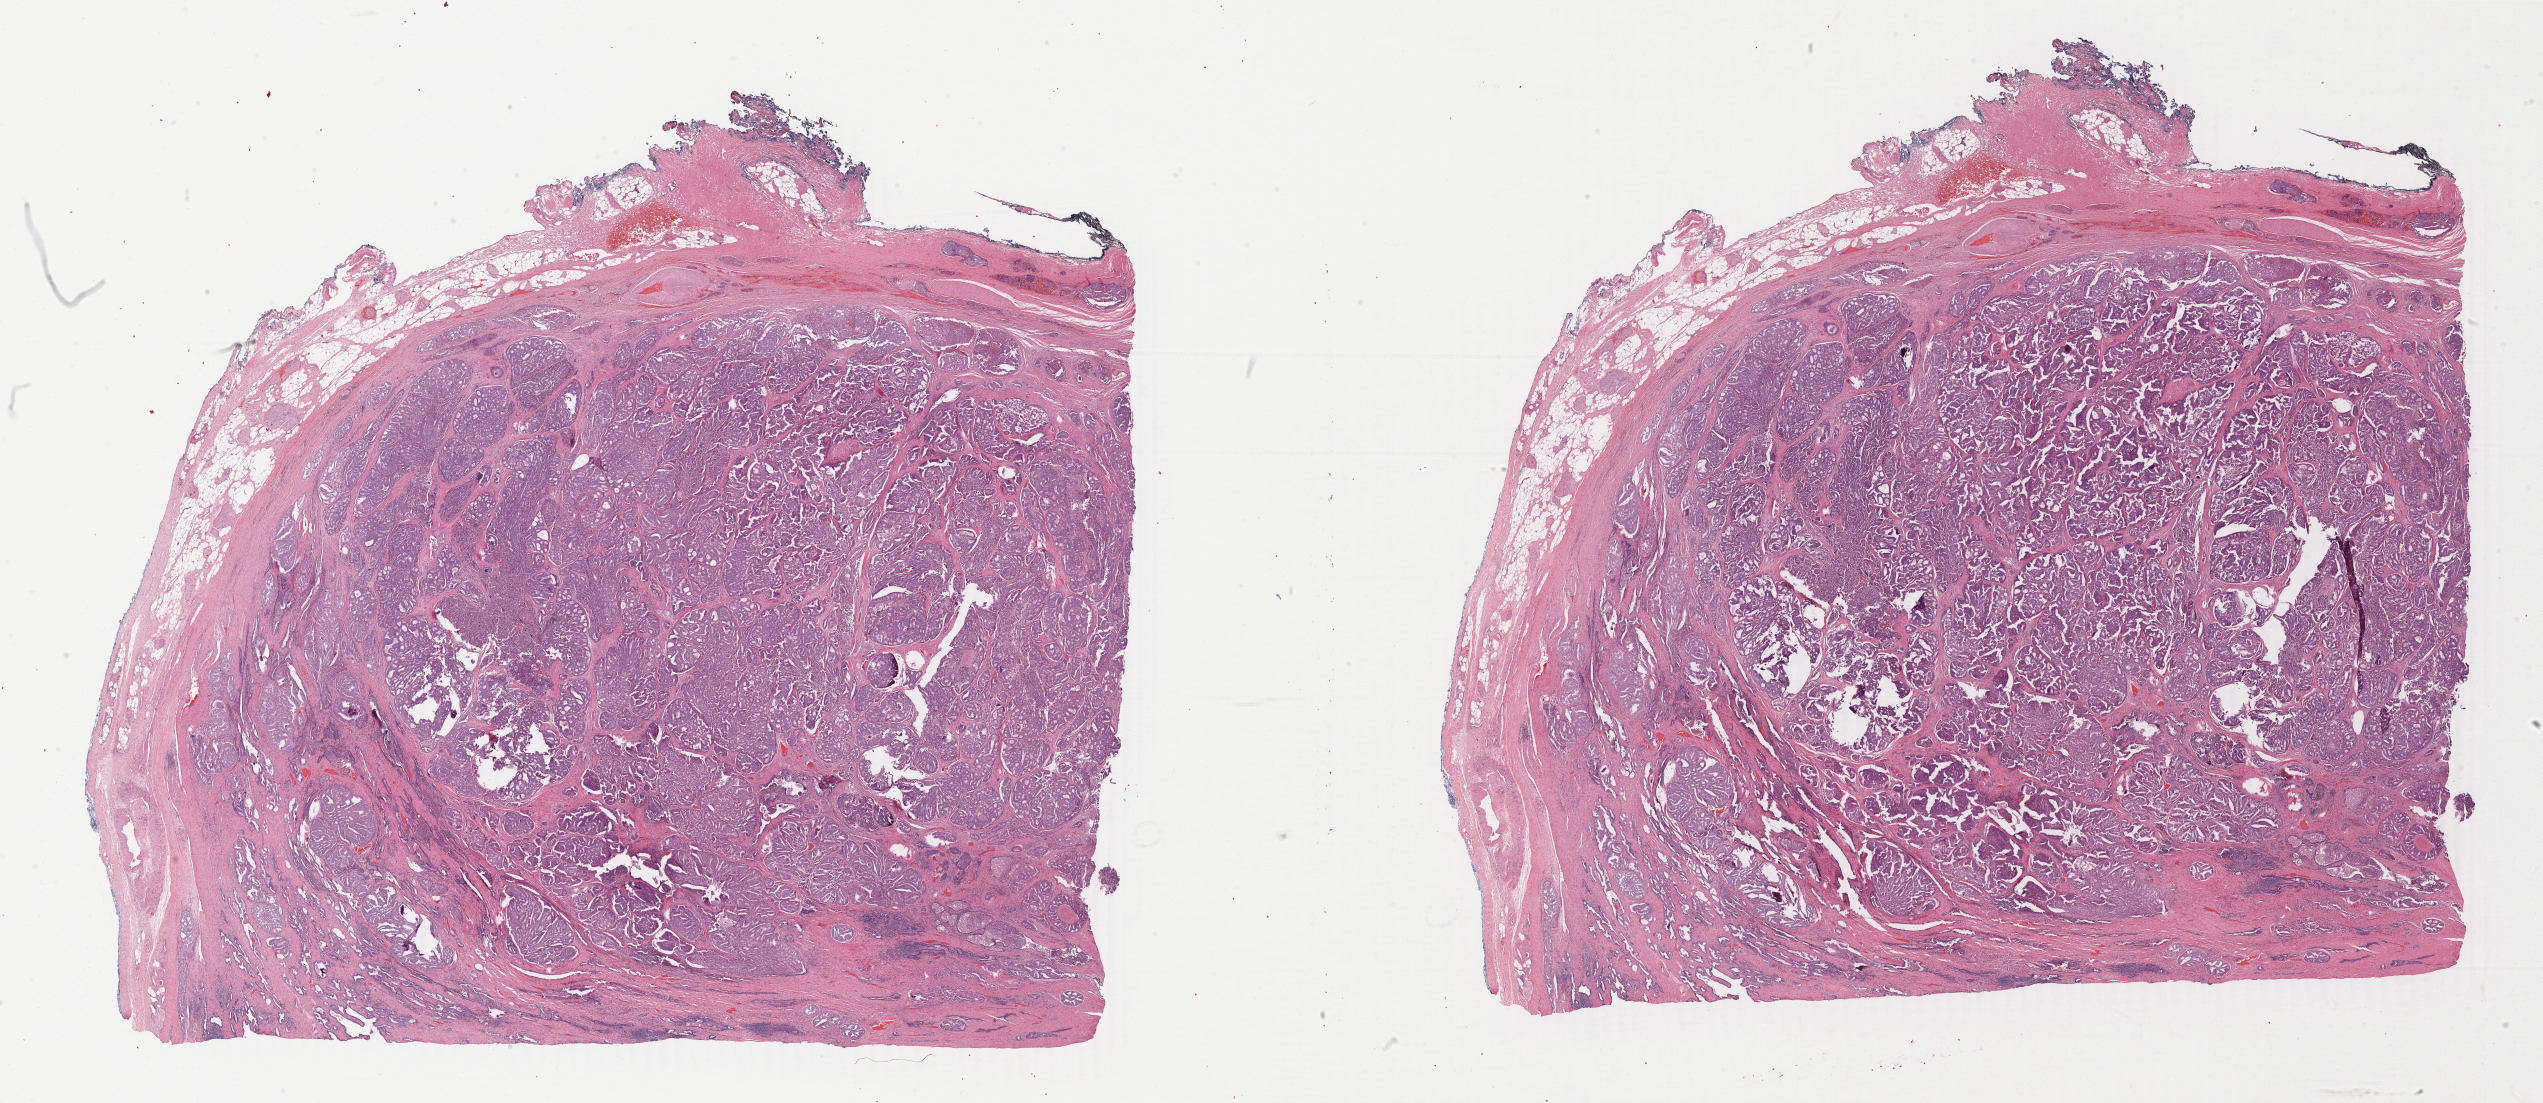
Whole-slide histology image, H&E, a low-resolution overview of the entire scanned area, about 40.5 x 17.5 mm; formalin-fixed paraffin-embedded (FFPE) diagnostic section; prostate, primary tumour sample. Male, age 57 years at initial diagnosis. Gleason score: 8 (4+4).
Laterality: bilateral. Lymph nodes positive (case pathology): 0 of 5 examined. Histologic diagnosis: Adenocarcinoma, NOS (prostate gland).